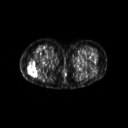
FDG PET of an extremity soft-tissue mass (from a PET/CT study), one axial slice. Position 25 of 267 along the scan axis. 3.27 mm slice thickness. 128 × 128 image matrix. Patient: female, 57 years. Case-level facts recorded for this patient, not image findings: histological type: epithelioid sarcoma with vascular differentiation; site of the primary tumour: right buttock.
Annotated regions visible in this slice (expert contour drawn on MRI and transferred to this co-registered scan by the dataset authors):
- gross tumour volume (mass): box from (x=29, y=62) to (x=35, y=74) px